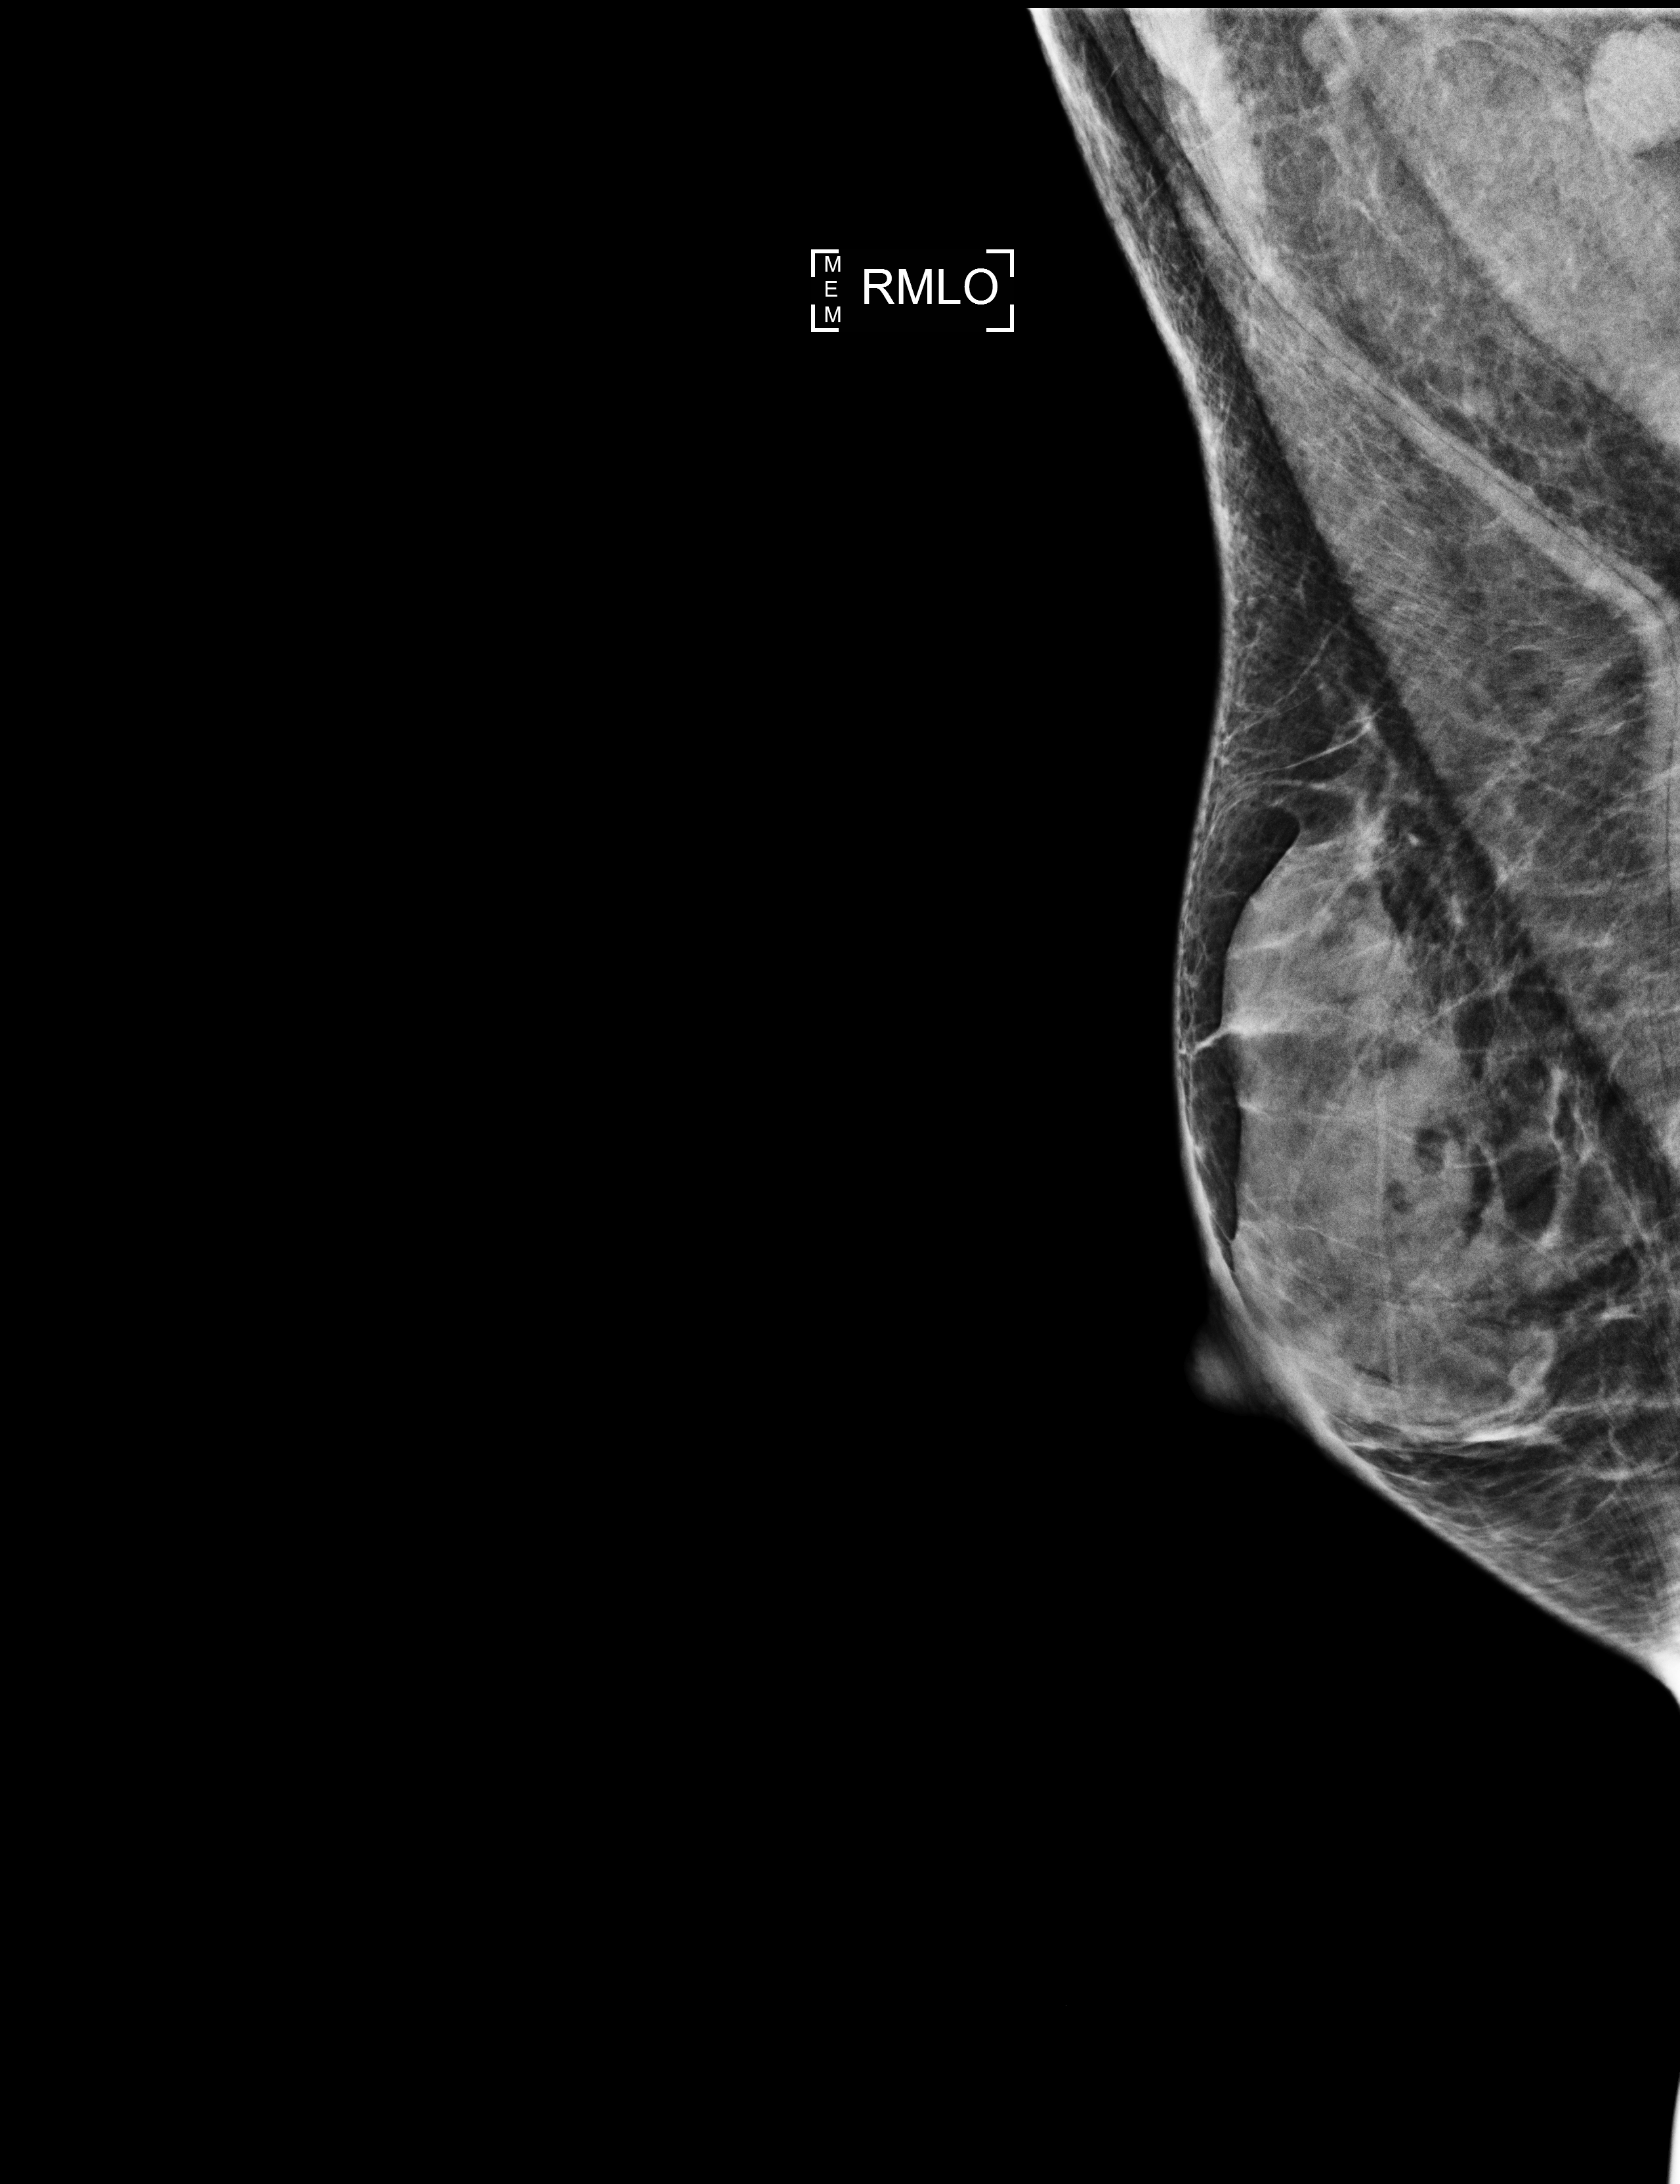
Full-field digital mammogram (FFDM); right breast; mediolateral oblique (MLO) view; annual screening mammography examination; compressed breast thickness 32 mm; system: Selenia Dimensions. Female patient, age 60 years.
Breast density at the screening exam (both breasts): heterogeneously dense (BI-RADS density category c). Final BI-RADS category for the screening round (tomosynthesis exam, both breasts): category 1. Recall: no recall after this screen.